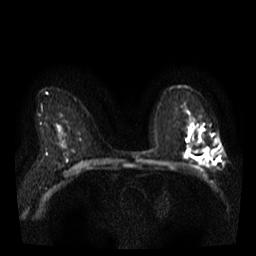
Breast MRI, one axial slice; diffusion-weighted series; image 2 of 4 stored at this slice position (different b-values; order by instance number); 3 T; 5 mm slice thickness; 256 × 256 image matrix. Female patient.
Outlined on this slice (outlined manually by an expert reader):
- tumour on diffusion-weighted imaging: bounding box (x1, y1, x2, y2) in pixels: (203, 147, 214, 160)